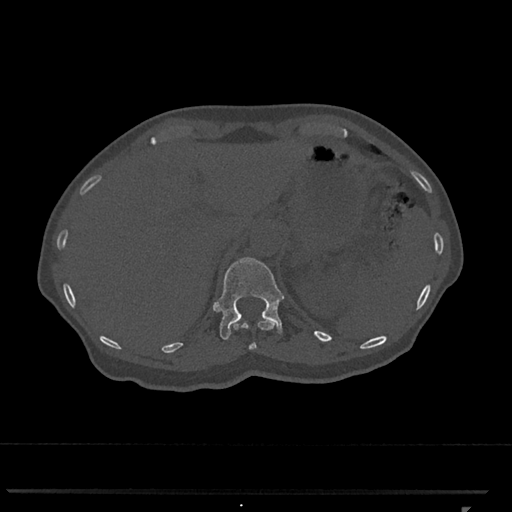
CT including the spine, one axial slice. Slice 481 of 793 in the series (ordered by position). Bone window (W 1800 / L 400 HU). 512 × 512 image matrix, field of view 380 × 380 mm. Patient: female, 62 years. From the clinical record (not read from this slice): primary cancer: renal.
Annotated regions visible in this slice (semi-automatic segmentation, software-assisted and operator-edited):
- T11 vertebra: bounding box (x1, y1, x2, y2) in pixels: (234, 319, 275, 350)
- T12 vertebra: (214, 257, 284, 340)